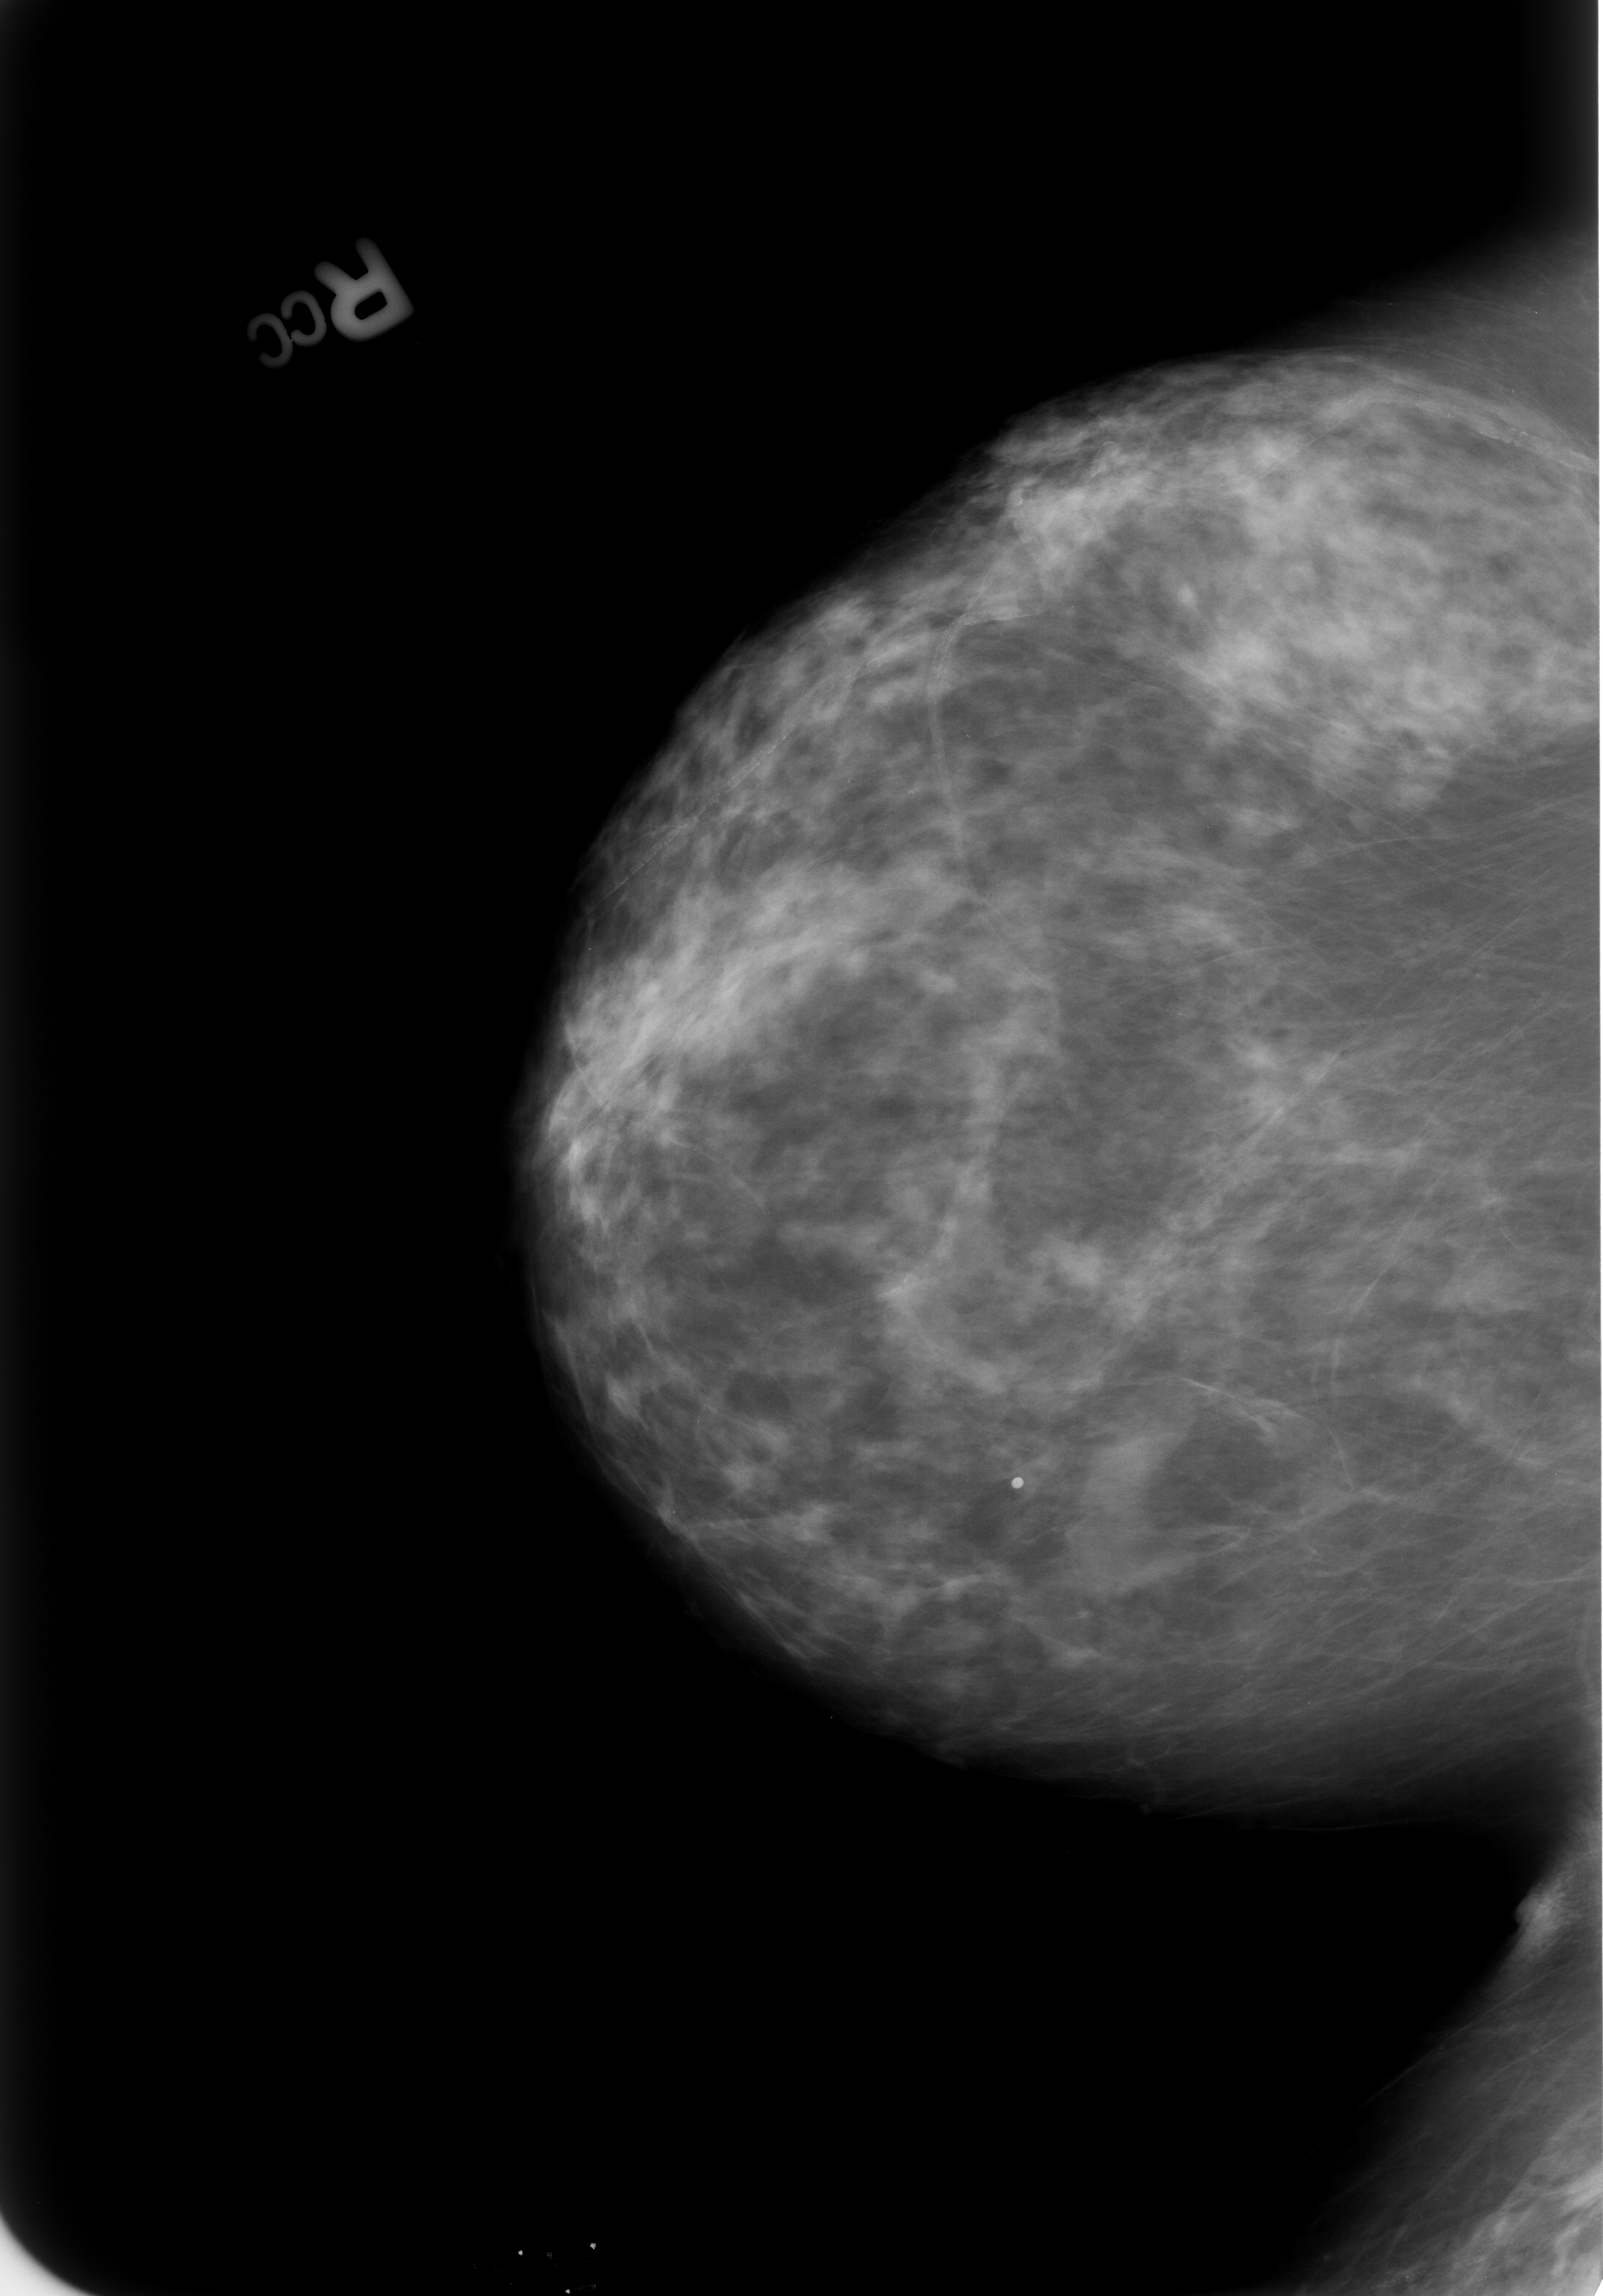
Scanned film-screen mammogram; right breast; craniocaudal (CC) view; BI-RADS breast density category 2 (scale 1–4).
Marked findings (only marked abnormalities are described; nothing is implied about the rest of the image): Finding 1 of 4: calcifications, morphology lucent center; BI-RADS assessment category 2; benign without callback (not worked up further). Finding 2 of 4: calcifications, morphology vascular; BI-RADS assessment category 2; benign; no additional work-up was recommended (benign without callback). Finding 3 of 4: calcifications, morphology vascular; BI-RADS assessment category 2; benign without callback (not worked up further). Finding 4 of 4: calcifications, morphology vascular; BI-RADS assessment category 2; subtlety rating 4 on a 1 (subtle) to 5 (obvious) scale; benign without callback (not worked up further).